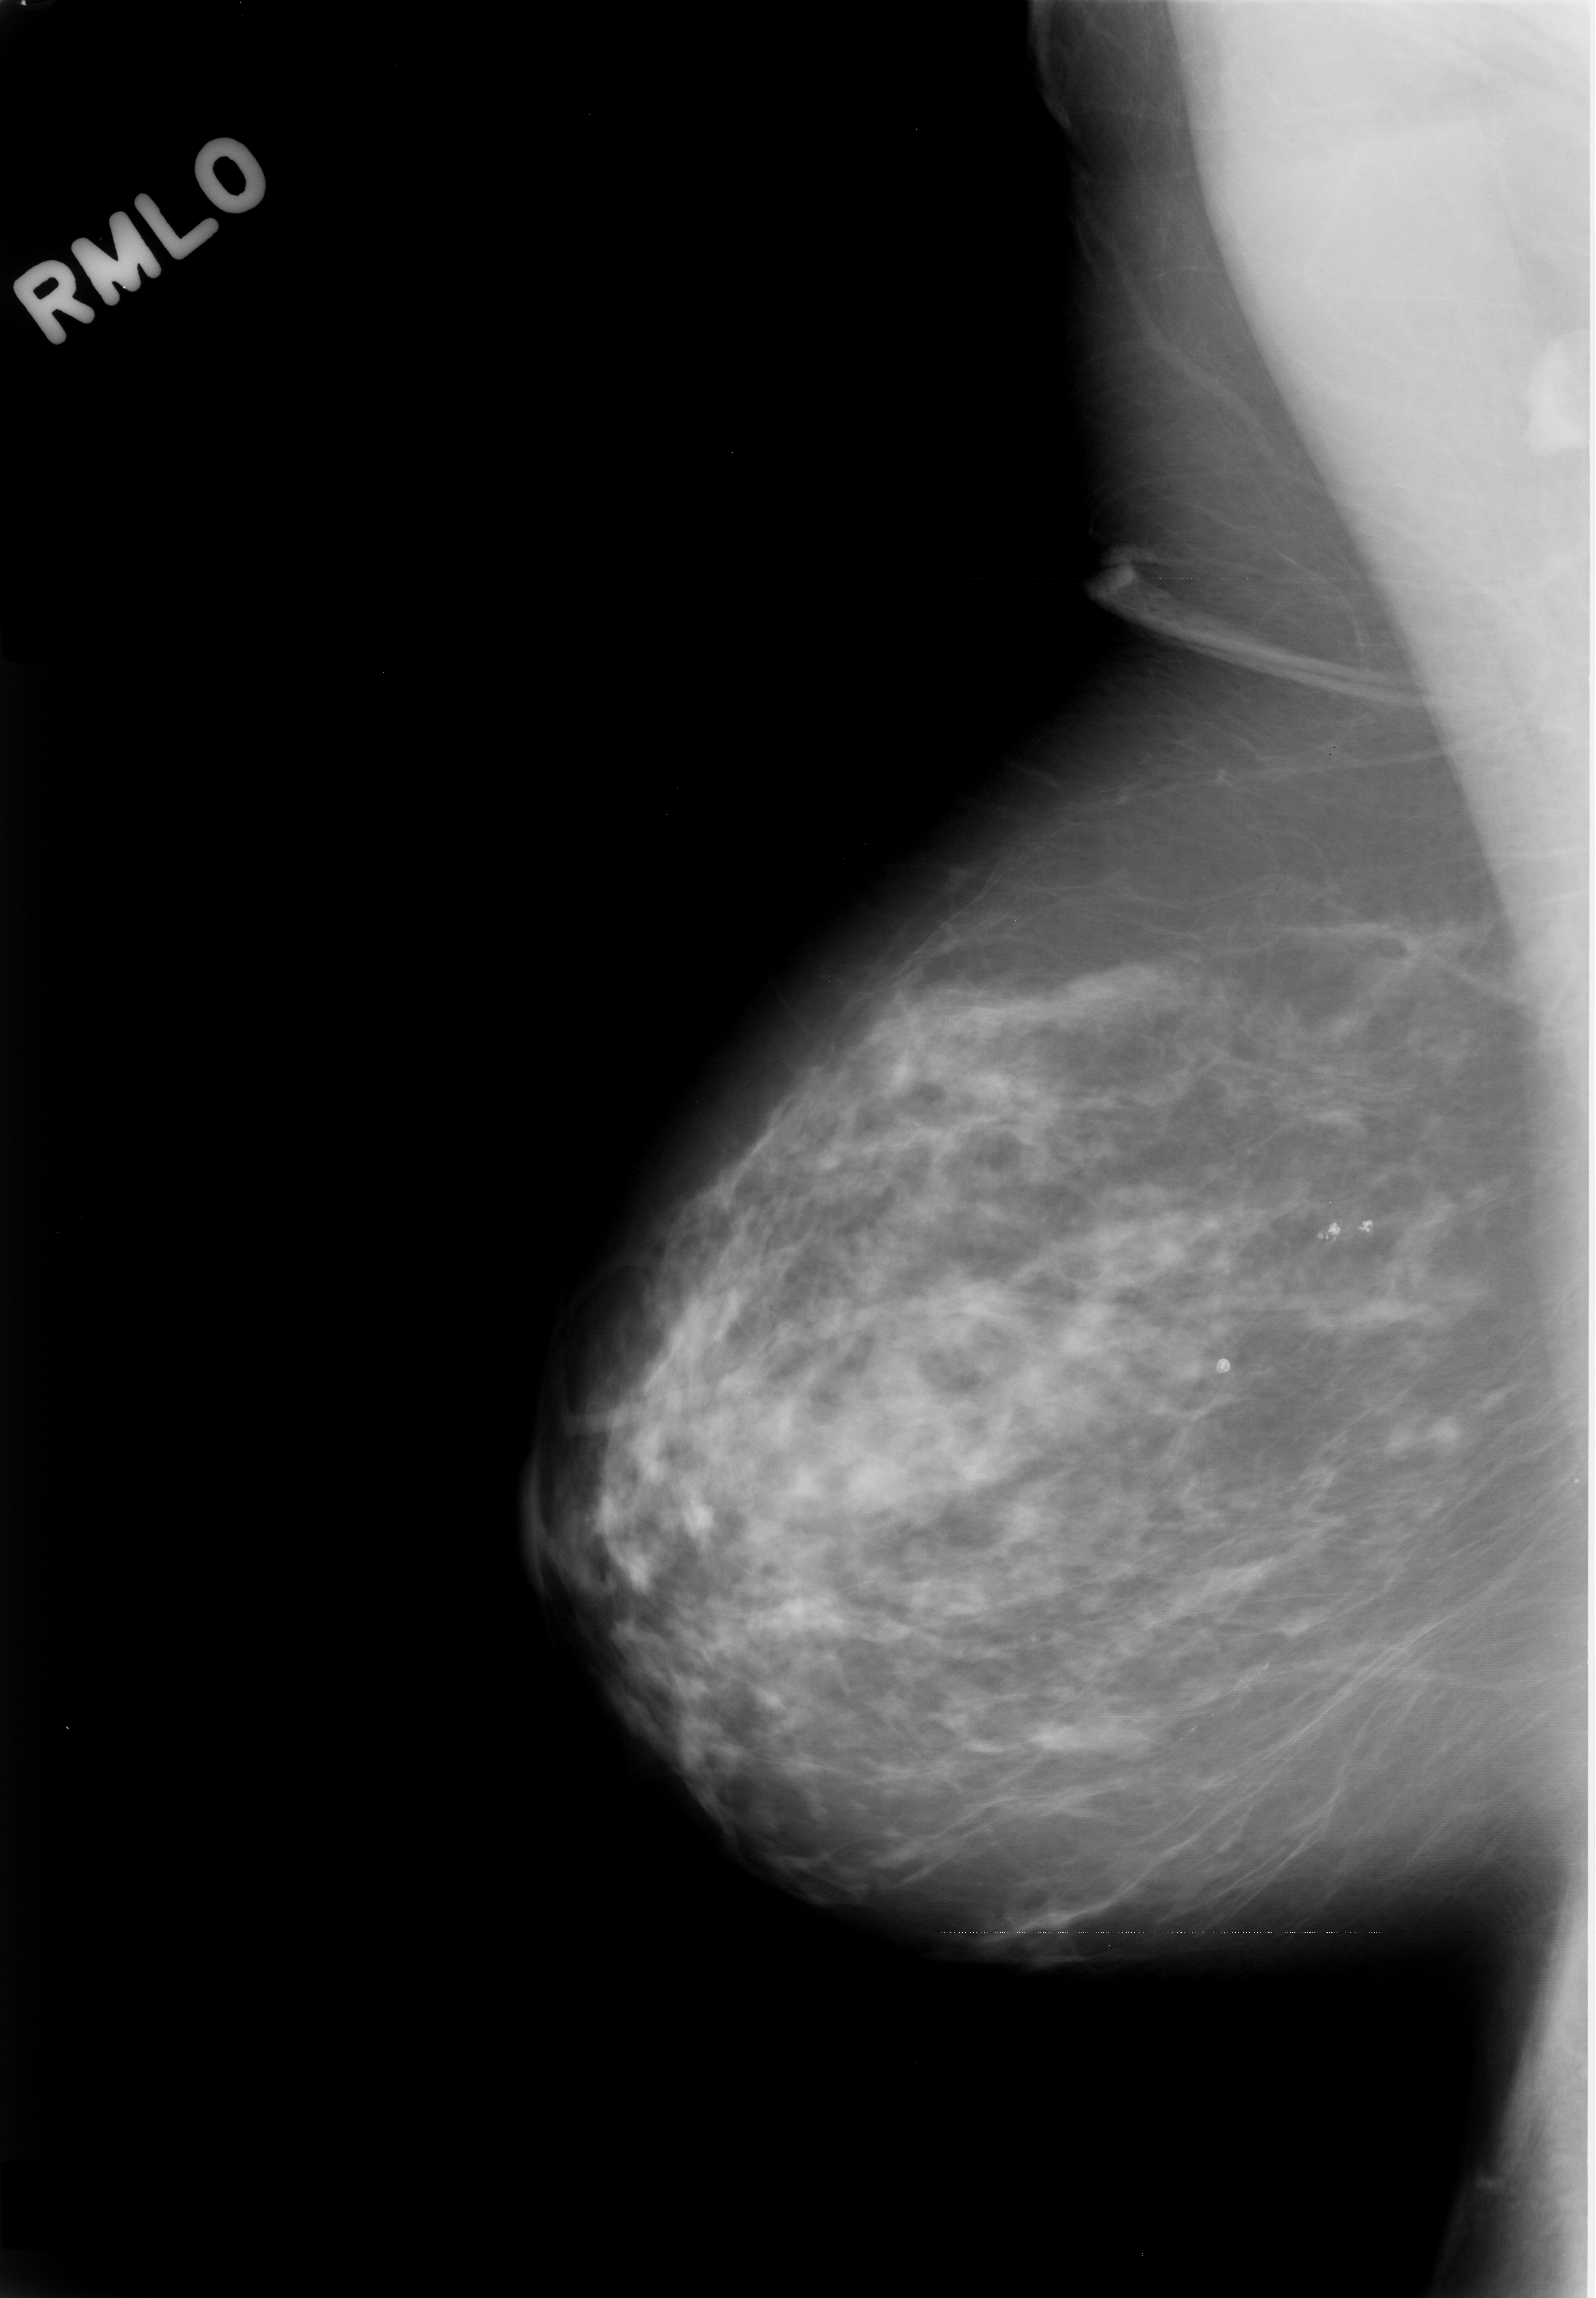
Mammogram (digitized film); right breast; MLO view; breast composition: scattered fibroglandular densities (BI-RADS density category 2 of 4); 1596 × 2298 image matrix.
Marked abnormalities (boxes around the expert regions of interest):
- calcifications, morphology fine linear branching, distribution linear; BI-RADS assessment category 4; subtlety rating 3 on a 1 (subtle) to 5 (obvious) scale; pathology result (as recorded, not read from the image): benign: bounding box [x1, y1, x2, y2] px = [1119, 1564, 1372, 1771]